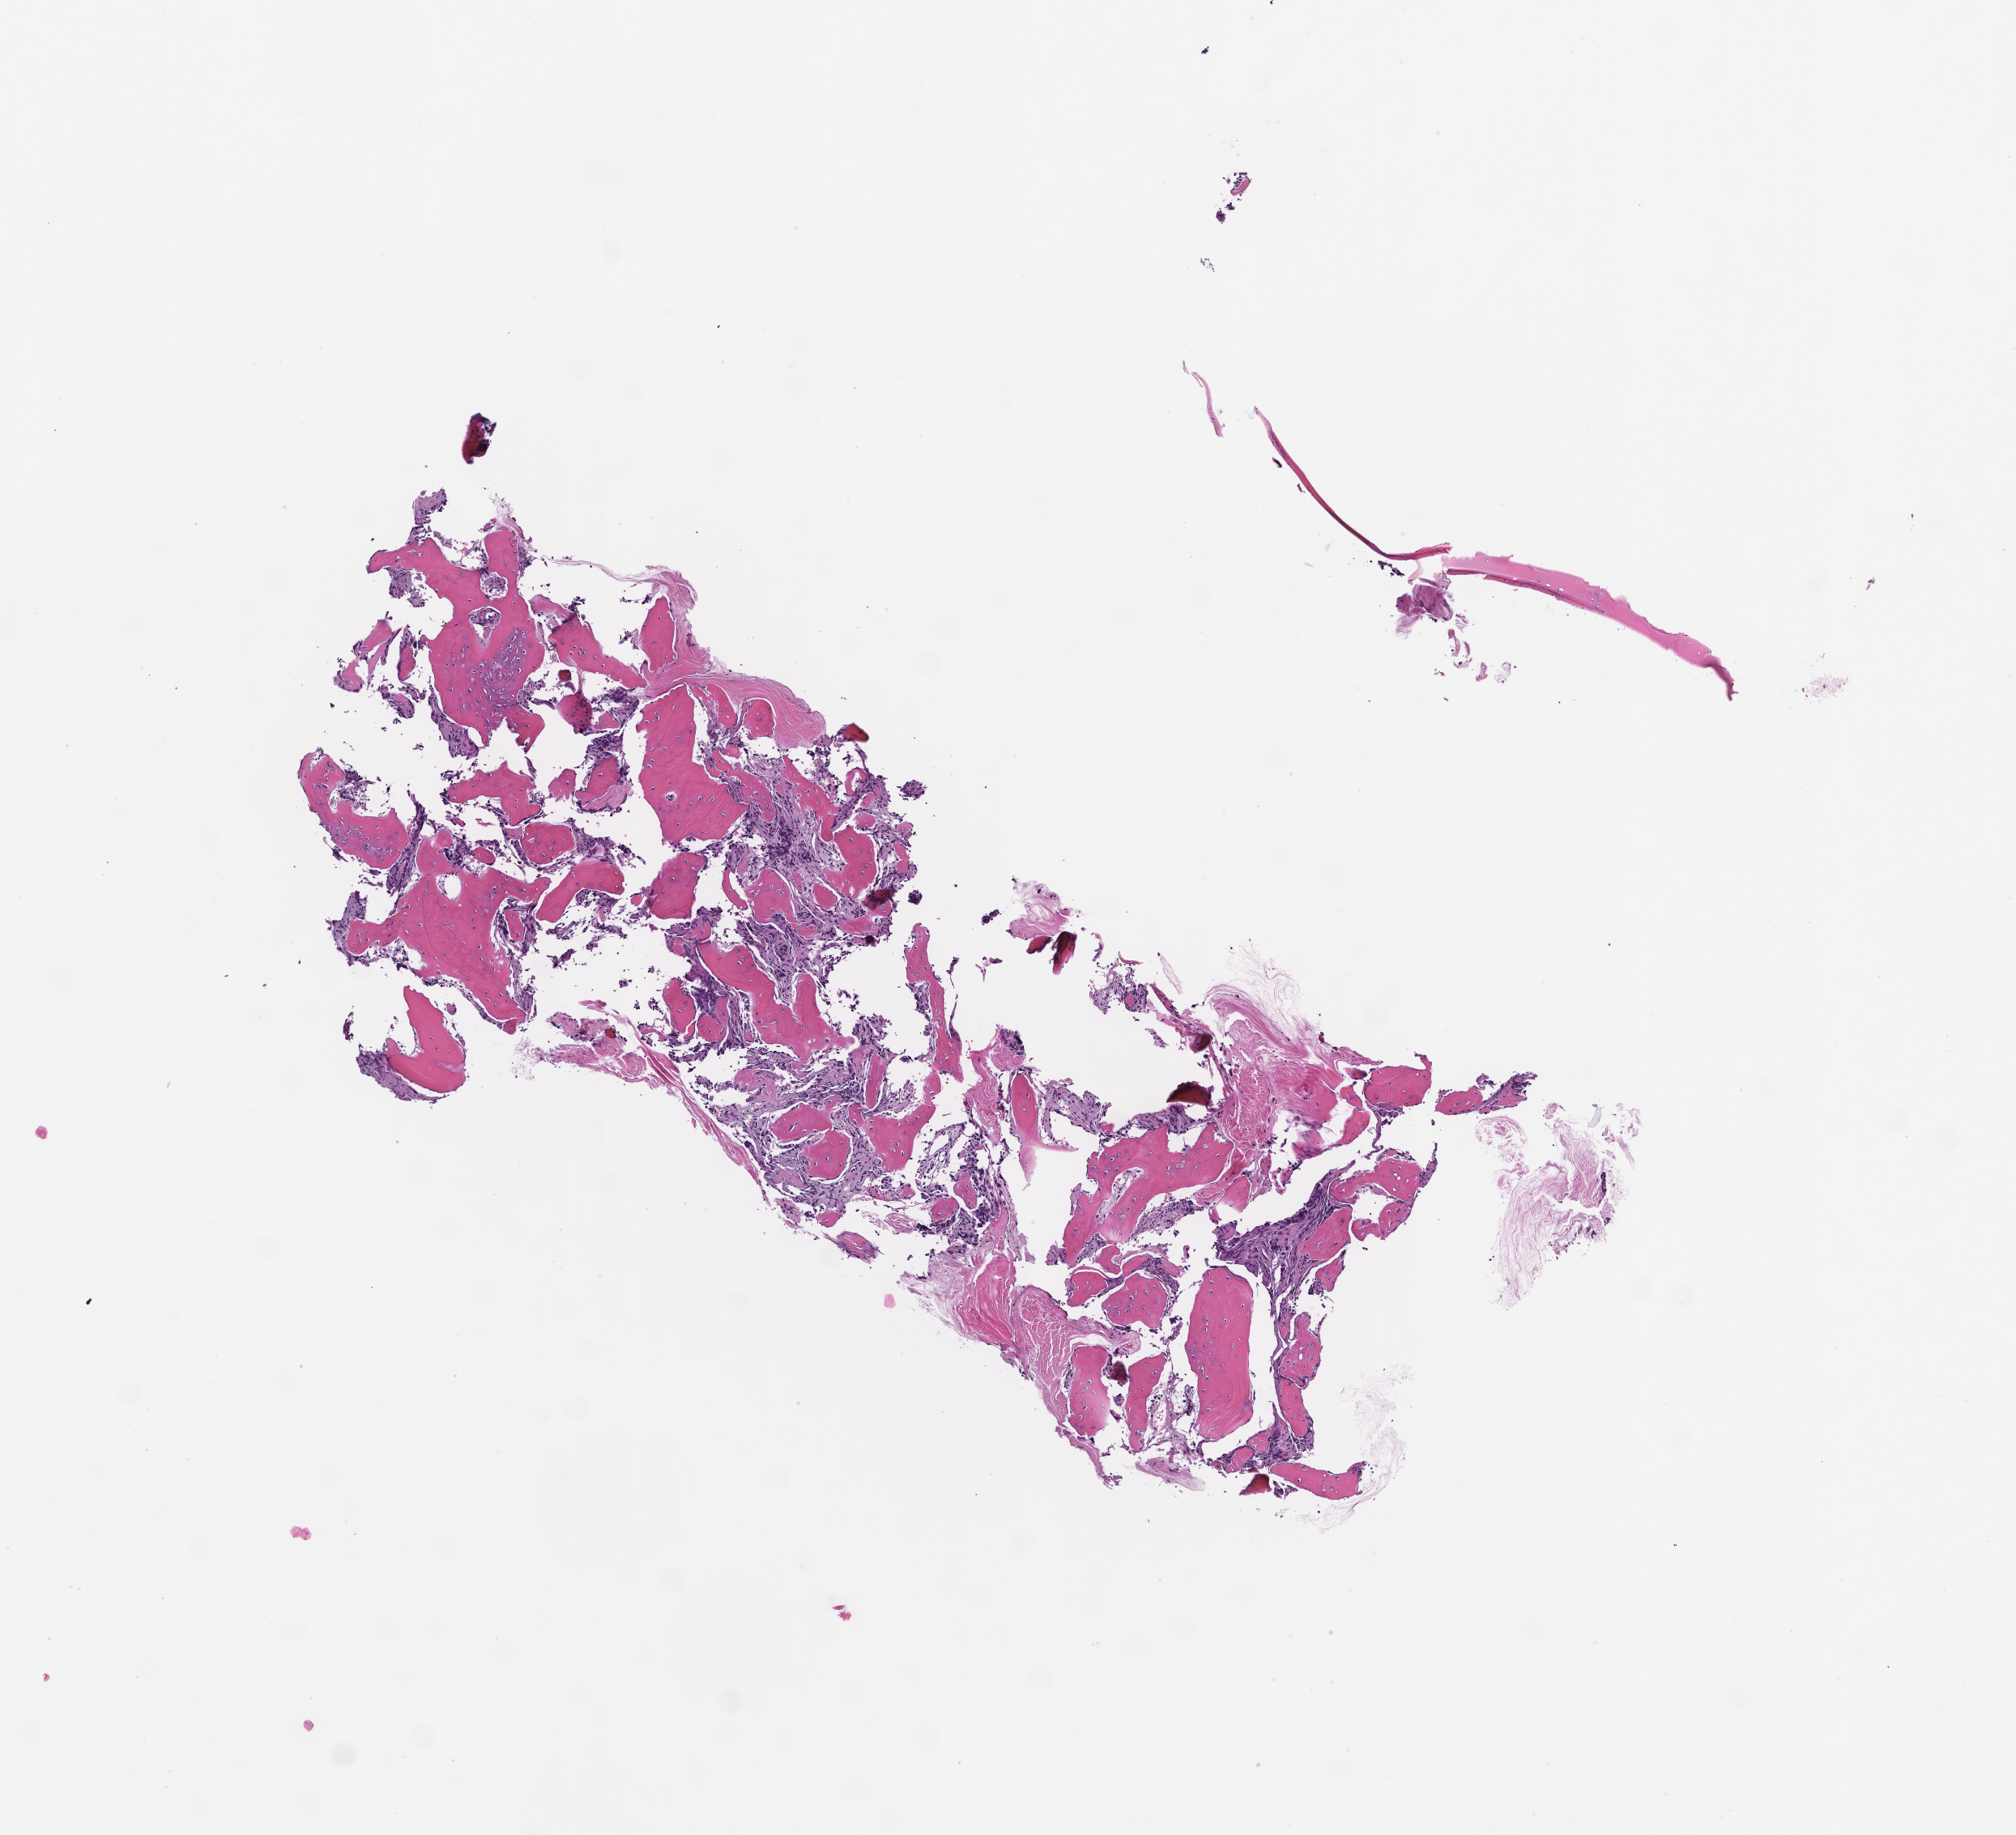
Digitized H&E-stained section, a low-resolution overview of the entire scanned area, about 5.0 x 4.6 mm. Formalin-fixed paraffin-embedded section. Archival tissue. Female patient.
• this section: metastasis (sampled organ not recorded)
• patient diagnosis (primary): Invasive Breast Carcinoma